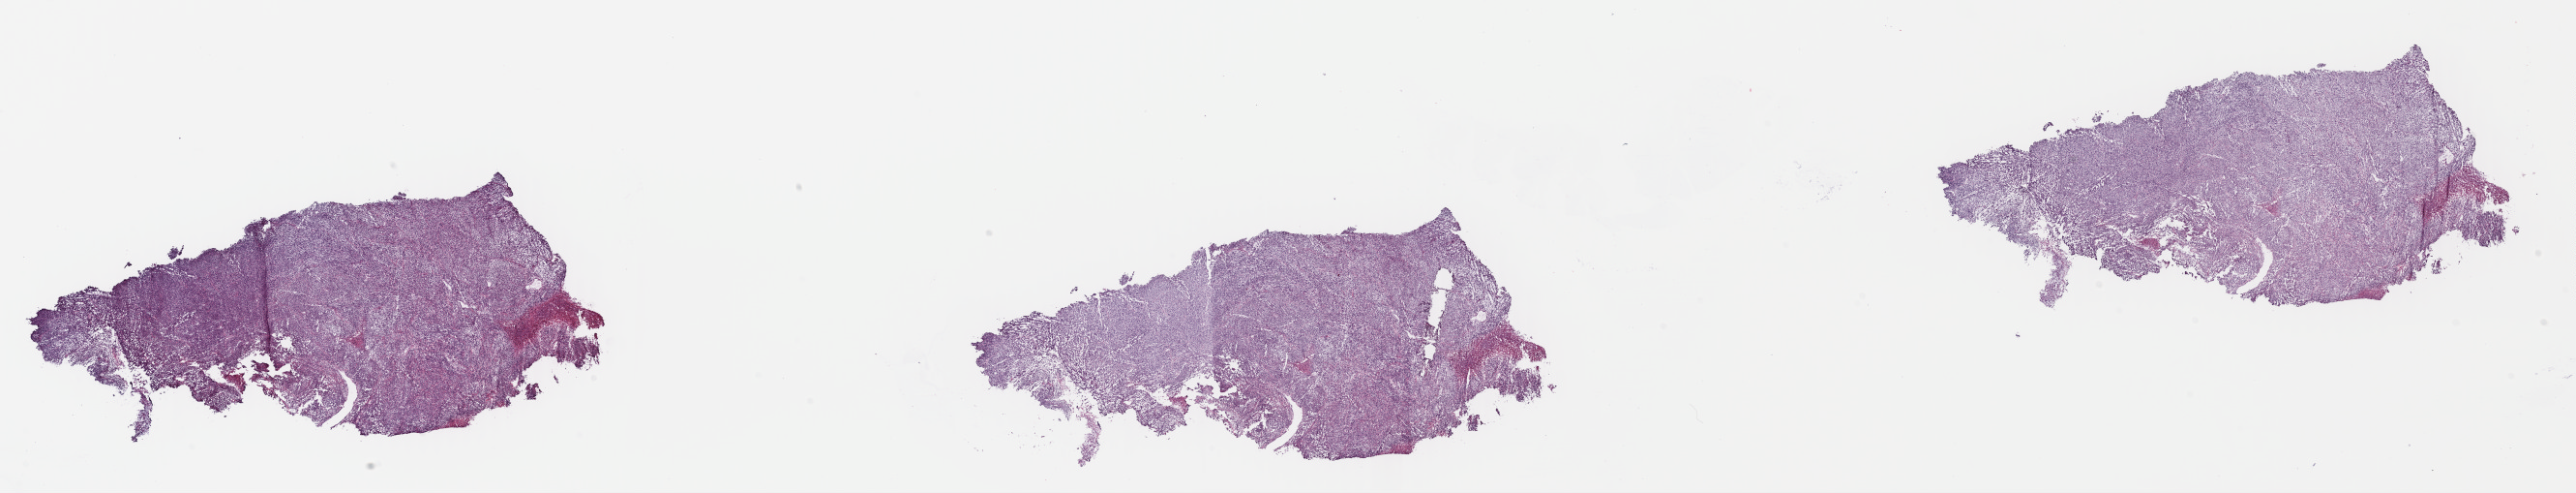
H&E-stained whole-slide image, a low-resolution overview of the entire scanned area, about 41.9 x 8.0 mm, frozen section from the top of the tissue portion, sample: primary tumour, connective, subcutaneous and other soft tissues. Female patient; age at initial diagnosis 68 years. Composition of this section per pathologist review: tumour cells 80%, tumour nuclei 80%, normal cells 0%, stromal cells 17%, necrosis 3%. Inflammatory infiltration, as recorded: lymphocyte infiltration 1%, monocyte infiltration 3%, neutrophil infiltration 1%.
Pathologic diagnosis: Fibromyxosarcoma.